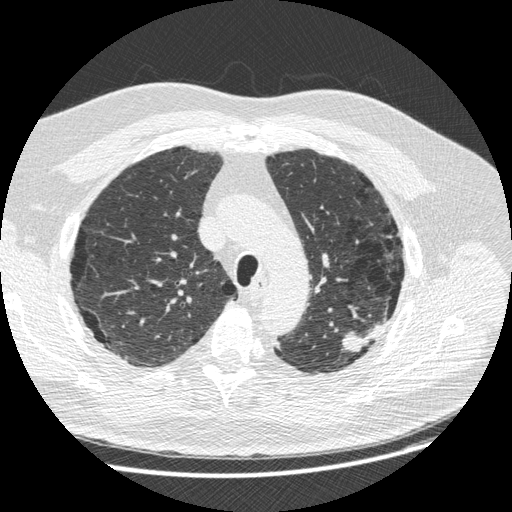
Low-dose screening chest CT, one axial slice. Position 198 of 258 along the scan axis. Reconstruction kernel STANDARD. Lung window (W 1500 / L -600 HU). 1.25 mm slice thickness. 512 × 512 image matrix, field of view 370 × 370 mm.
Structures marked on this image (expert manual segmentation):
- lesion 1 (tumor, upper lobe of left lung): bounding box (x1, y1, x2, y2) in pixels: (342, 323, 383, 352)